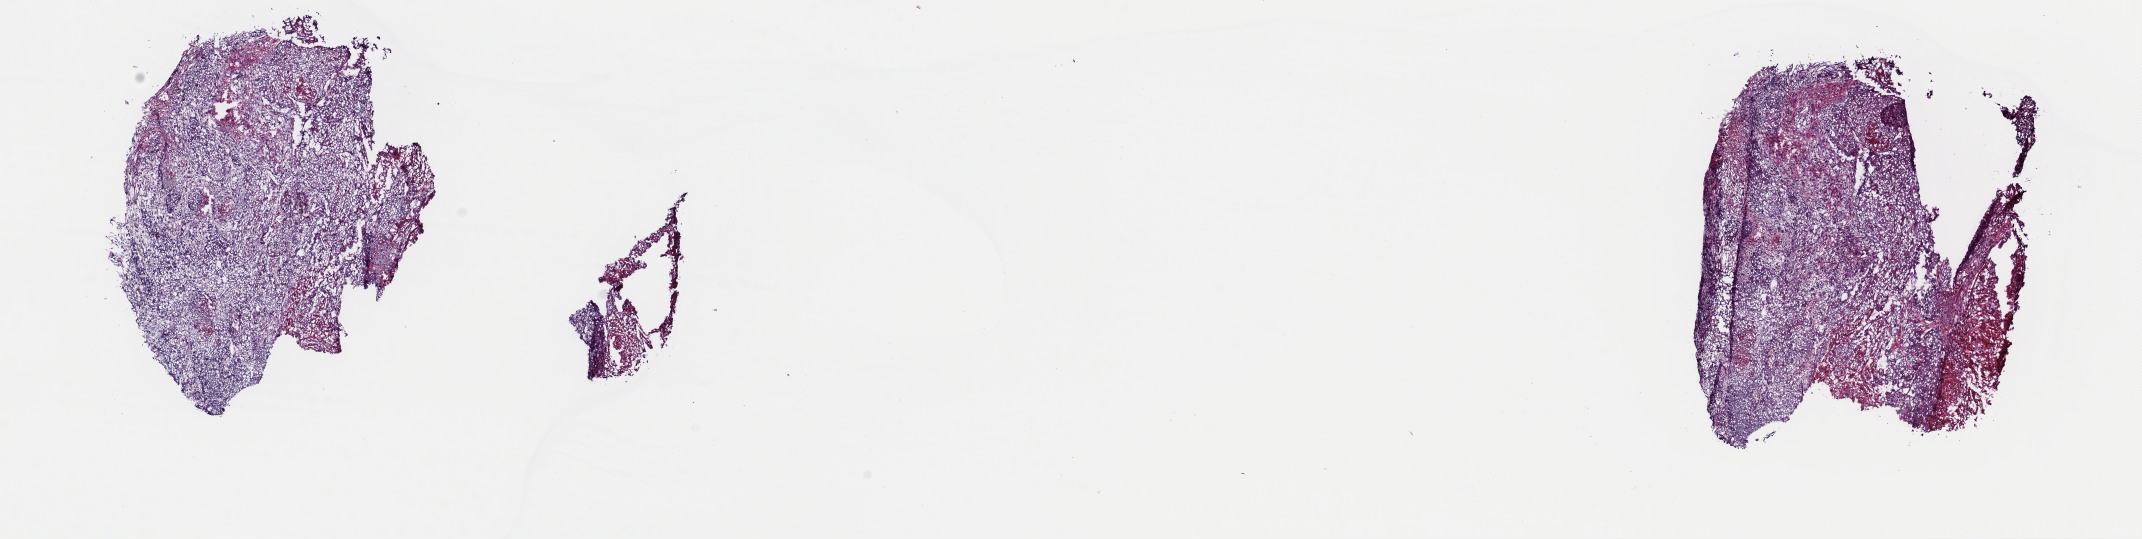
H&E-stained whole-slide image, whole scanned area (about 16.9 x 4.3 mm) shown as a low-resolution overview. Frozen section. Sample: primary tumour, head and neck. Male patient; age at initial diagnosis 47 years. Histologic grade: G2 (moderately differentiated). Pathologist review of this section (percent, as recorded): tumour cells 60%, tumour nuclei 70%, normal cells 0%, stromal cells 30%, necrosis 10%. Infiltration values recorded for this section: lymphocyte infiltration 10%, monocyte infiltration 0%, neutrophil infiltration 0%.
- AJCC pathologic stage: IVA (7th edition)
- diagnosis: Squamous cell carcinoma, NOS (mouth, NOS)
- lymph nodes positive (case pathology): 1 of 30 examined